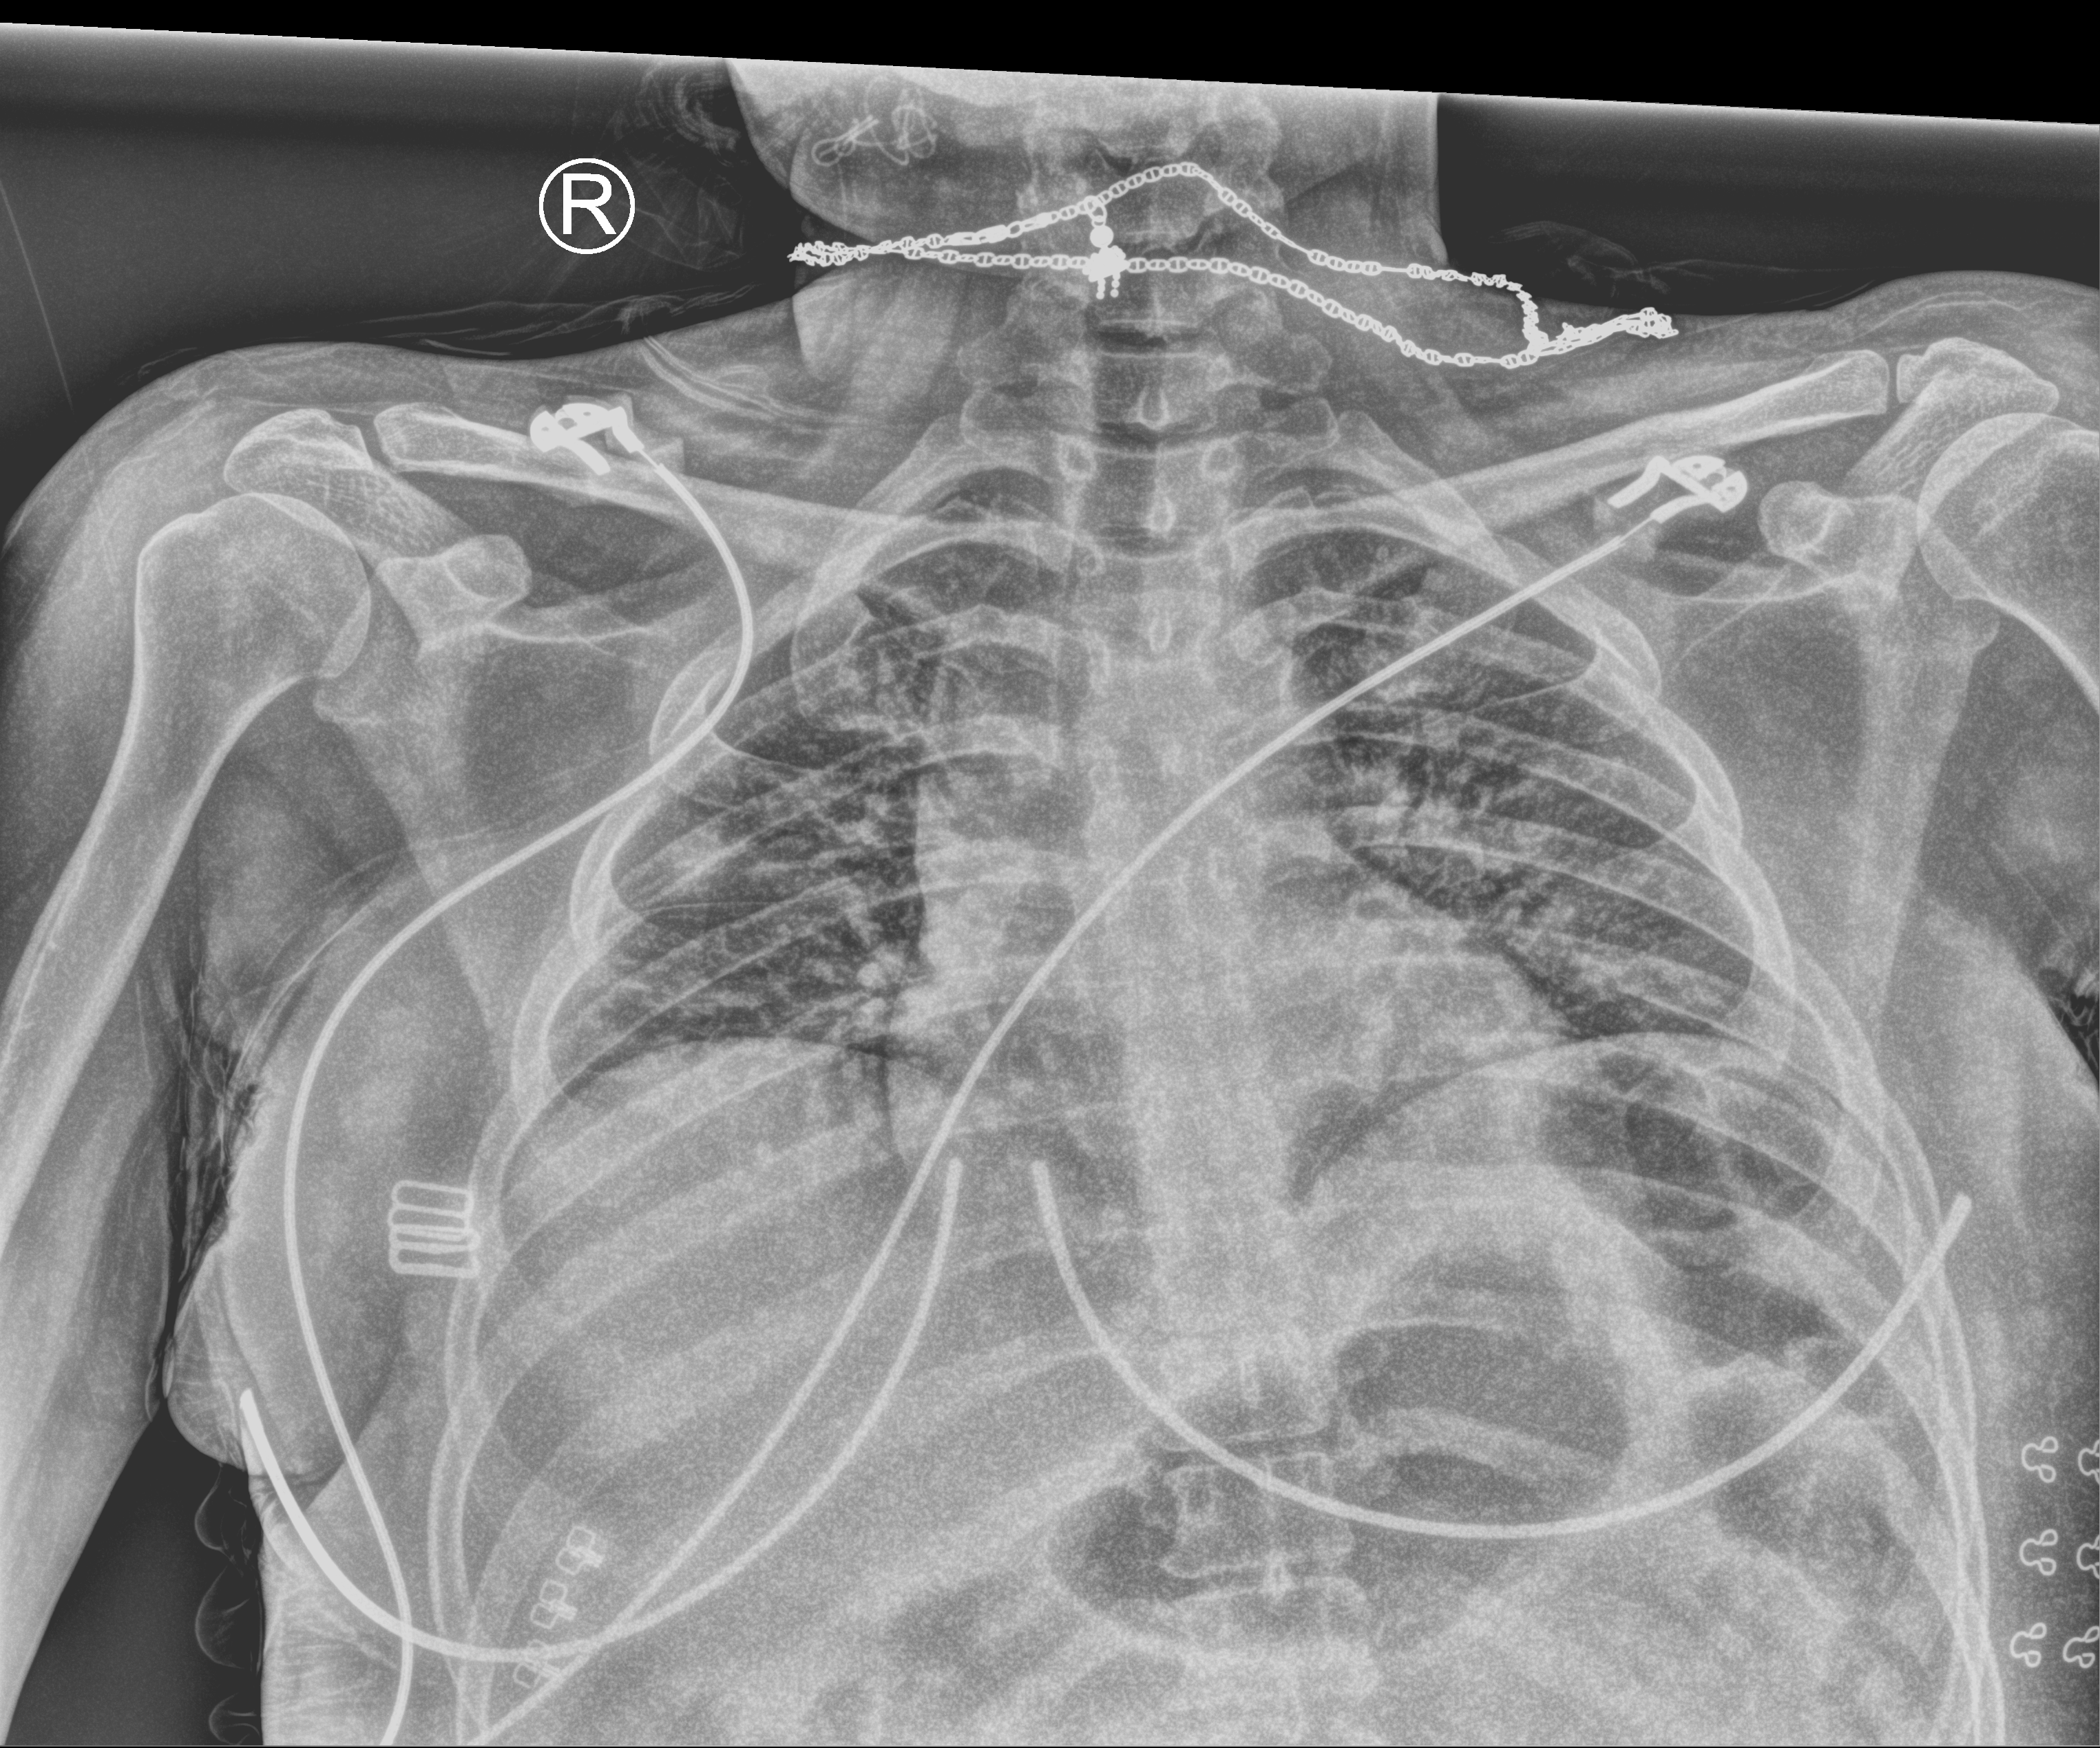
Portable chest radiograph. Female patient hospitalised with COVID-19, age 18–59 years.
Hospital-stay facts (about this admission, not read from this image; timing relative to this image not recorded): COPD (admission record): no; chronic kidney disease (admission record): no.